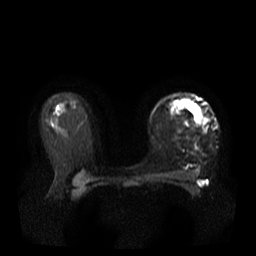
Breast MRI, one axial slice. Position 25 of 37 along the scan axis. Diffusion-weighted series; image 2 of 4 stored at this slice position (different b-values; order by instance number). 3 T. 5 mm slice thickness. 256 × 256 image matrix, field of view 380 × 380 mm. Female patient.
Structures marked on this image (outlined manually by an expert reader):
- tumour on diffusion-weighted imaging: bounding box [x1, y1, x2, y2] px = [197, 115, 205, 125]